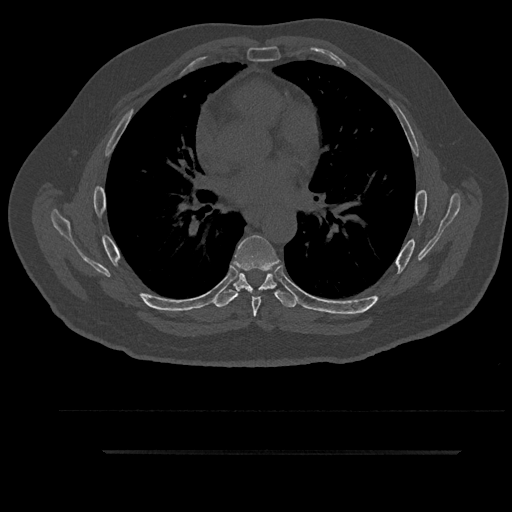
CT including the spine, one axial slice. 120 kVp. Bone window (W 1800 / L 400 HU). 0.5 mm slice thickness. 512 × 512 image matrix, field of view 432 × 432 mm. Male patient, age 63 years. From the clinical record (not read from this slice): primary cancer: renal; vertebrae with lytic lesions (as recorded): T8.
Outlined on this slice (semi-automatic segmentation, software-assisted and operator-edited):
- T5 vertebra: bounding box [x1, y1, x2, y2] px = [260, 286, 266, 289]
- T6 vertebra: [233, 235, 279, 317]
- T7 vertebra: [214, 273, 299, 308]